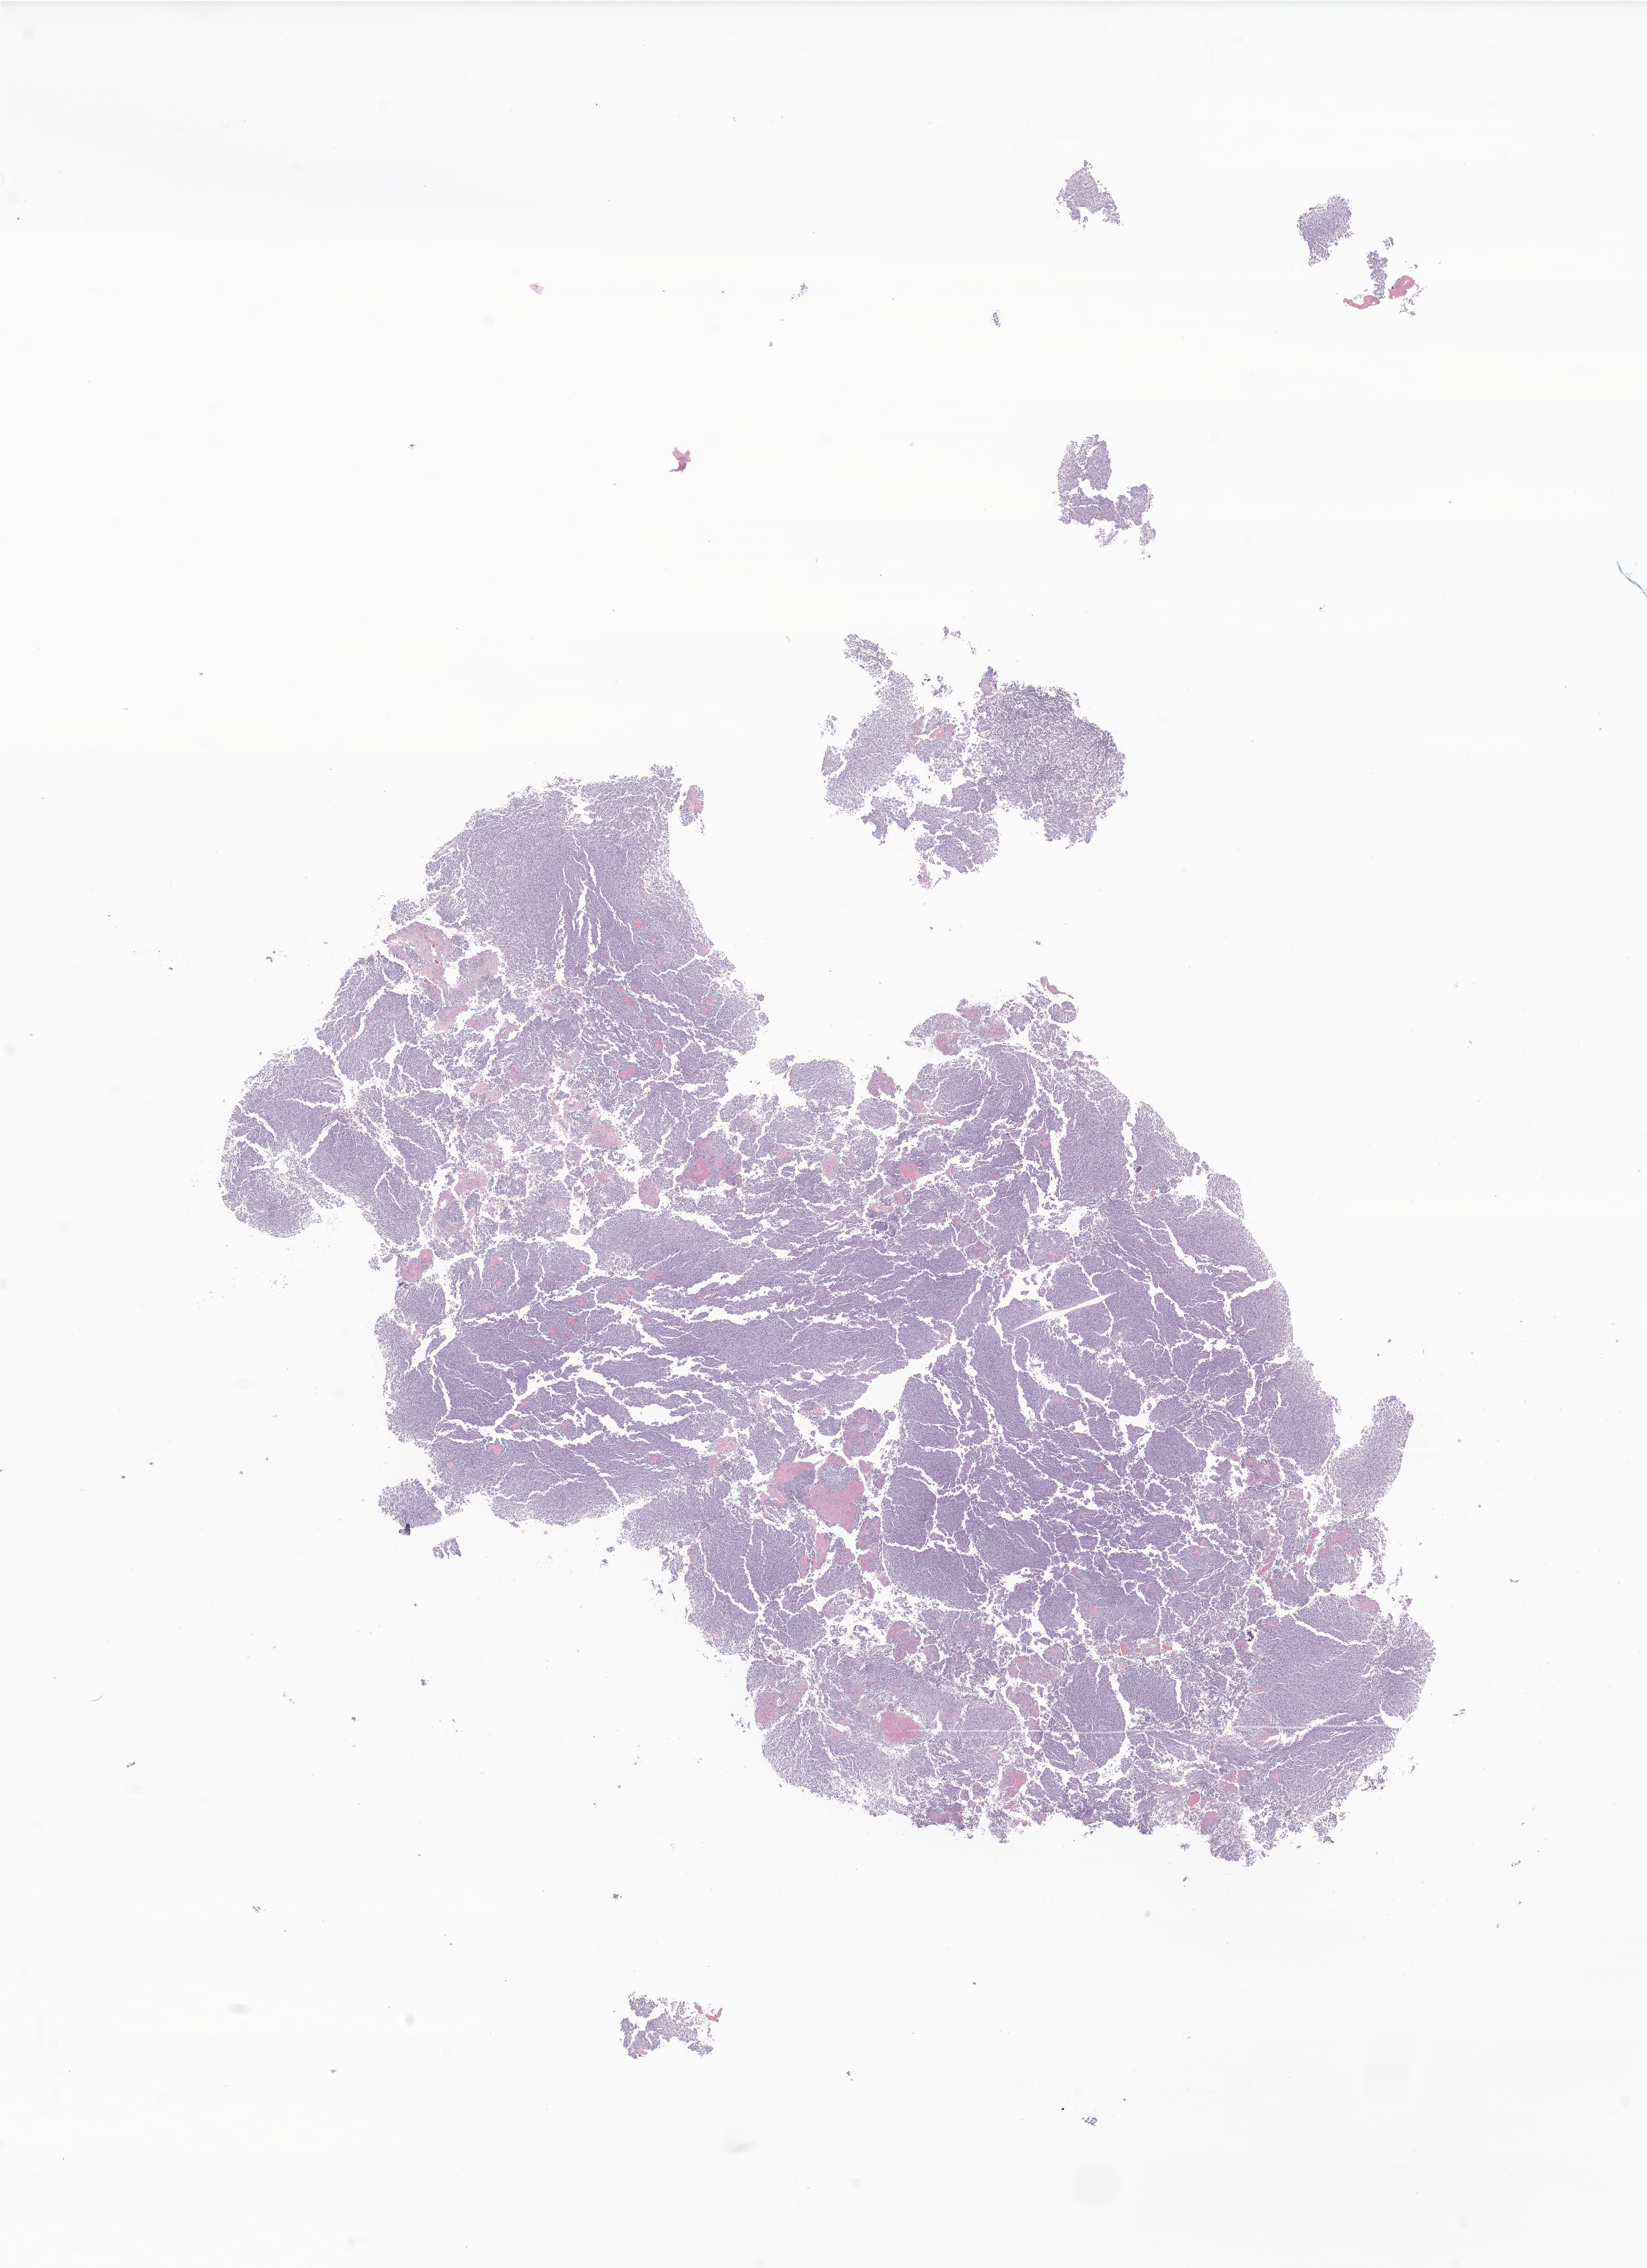
Whole-slide image, hematoxylin and eosin (H&E) stain of tumor tissue from the brain stem — whole scanned area (about 15.1 x 20.8 mm) shown as a low-resolution overview; FFPE section. Male patient, age 212 months.
Diagnosis (ICD-O-3 morphology term): Glioma, malignant.